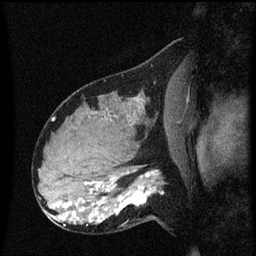
Breast MRI (dynamic contrast-enhanced), one sagittal slice. Dynamic contrast-enhanced series, image 2 of 3 at this slice position (ordered by acquisition). 1.5 T. TE 4.2 ms, TR 8.4 ms. 256 × 256 image matrix, field of view 200 × 200 mm. Patient: female, 31 years. From the clinical record (not read from this slice): setting: breast cancer imaged before/during neoadjuvant chemotherapy; receptor status: HR-positive, HER2-negative.
Structures marked on this image (semi-automatically segmented with operator editing):
- analysis volume of interest (the breast-tissue region the enhancement analysis was run in; not a lesion): bounding box [x1, y1, x2, y2] px = [102, 166, 168, 225]
- tumour enhancement mask (voxels above the 70 % enhancement threshold inside the analysis volume of interest): [102, 172, 156, 223]